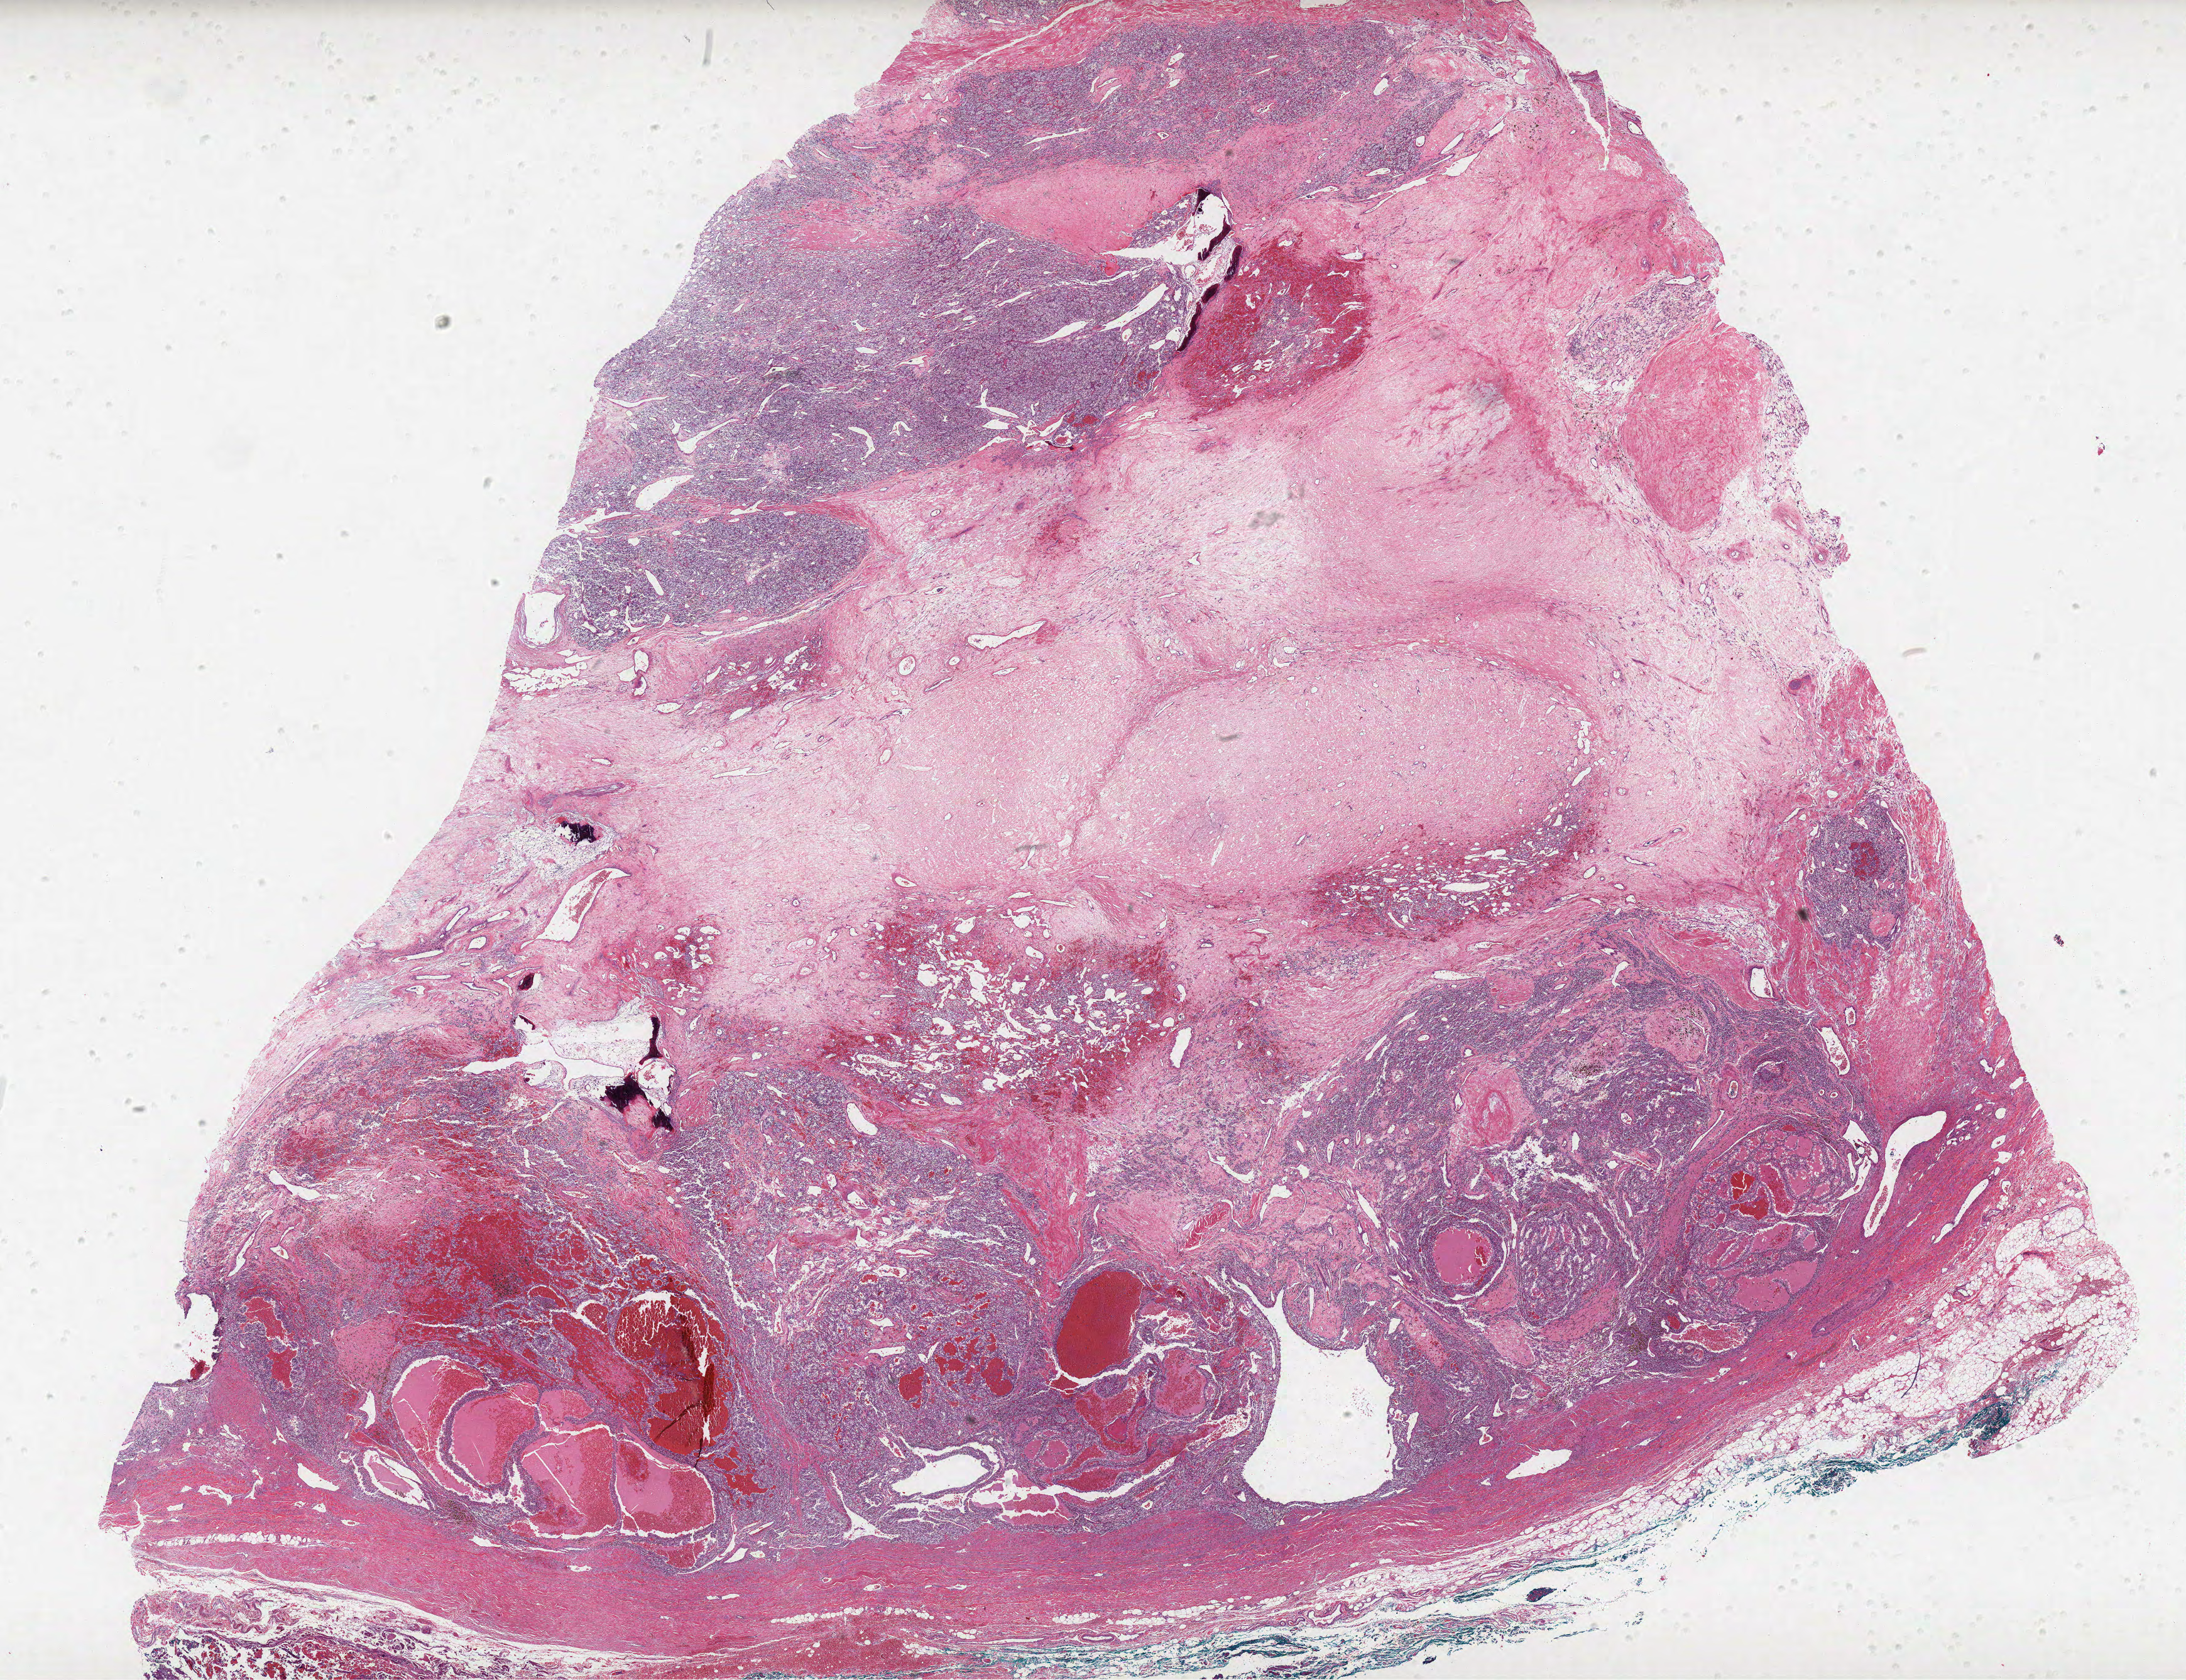
Whole-slide histology image, Hematoxylin and eosin (H&E) stained — shown as a low-resolution overview of the whole scanned area (about 27.8 x 21.4 mm, acquisition: 40x scan), FFPE section, primary tumour sample from the kidney. Male, age 40 years at initial diagnosis. Histologic grade: G3 (poorly differentiated).
AJCC pathologic stage: I. Histologic diagnosis: Clear cell adenocarcinoma, NOS. TNM: T1b N0 M0. Lymph nodes positive (case pathology): 0 of 3 examined.